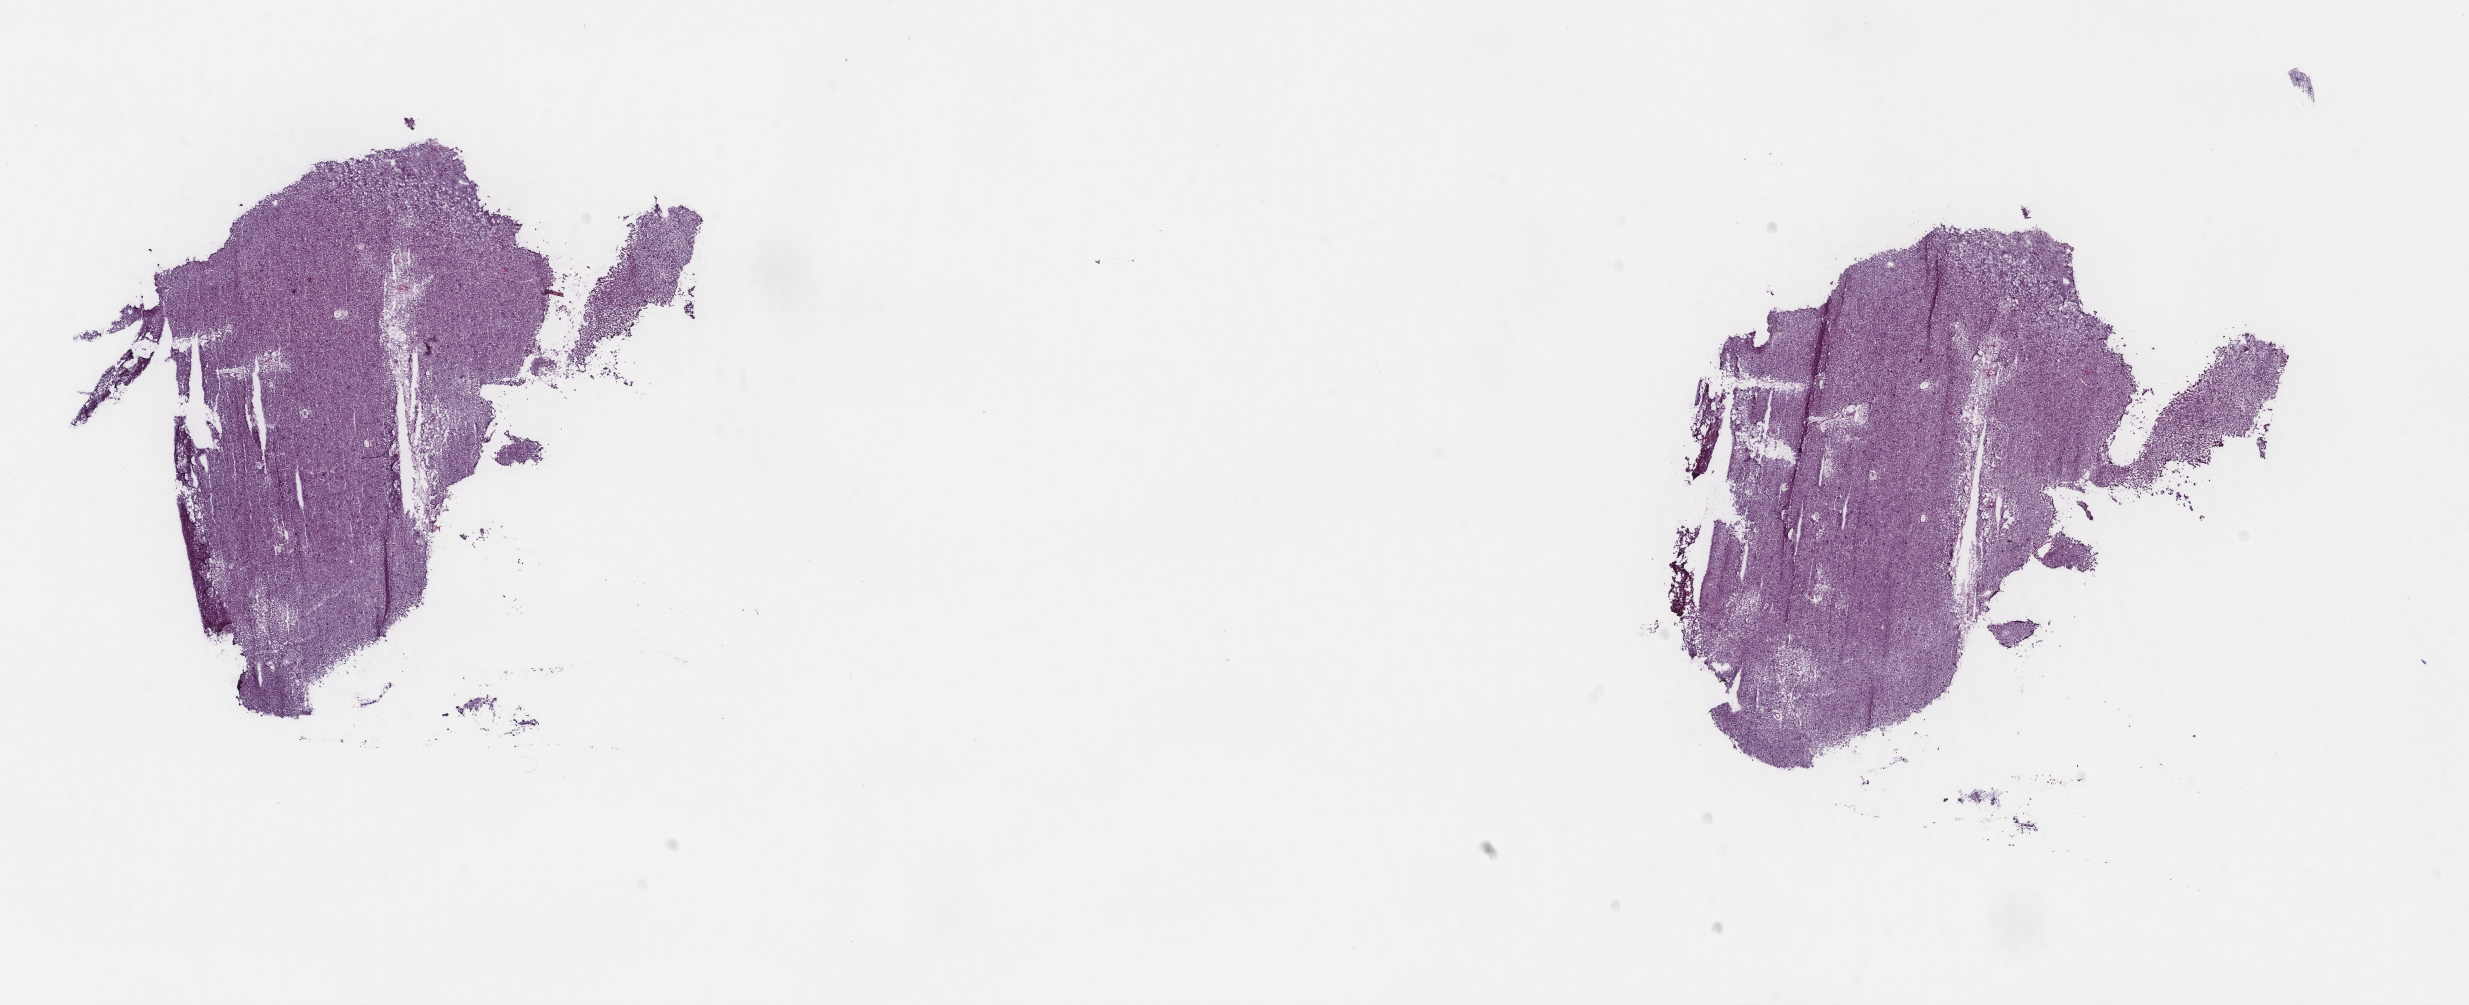
Digitized H&E-stained tissue section (whole slide), whole scanned area (about 19.6 x 8.0 mm) shown as a low-resolution overview. Frozen section from the top of the tissue portion. Sample: primary tumour, brain. Patient: female, age at initial diagnosis 33 years. Histologic grade: G3 (poorly differentiated). Composition of this section per pathologist review: tumour cells 30%, tumour nuclei 70%, normal cells 30%, stromal cells 40%, necrosis 0%. Inflammatory infiltration, as recorded: lymphocyte infiltration 0%, monocyte infiltration 0%, neutrophil infiltration 0%.
Pathologic diagnosis: Astrocytoma, anaplastic (cerebrum). Laterality: right.